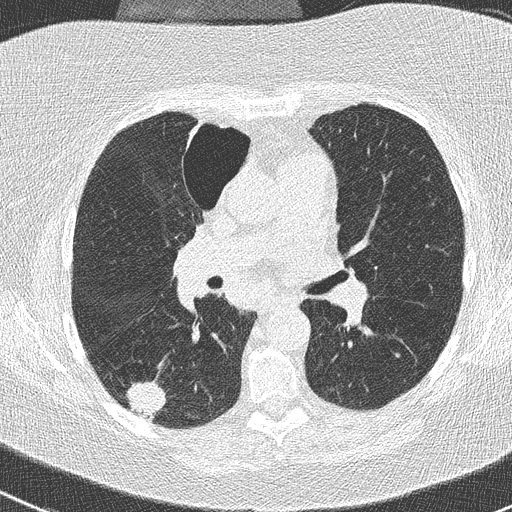
Low-dose screening chest CT, one axial slice. Slice 147 of 261 in the series (ordered by position). 120 kVp. Lung window (W 1500 / L -600 HU). 2 mm slice thickness. 512 × 512 image matrix, field of view 310 × 310 mm.
Outlined on this slice (outlined manually by an expert reader):
- lesion 1 (tumor, lower lobe of right lung): bounding box (x1, y1, x2, y2) in pixels: (126, 381, 166, 420)